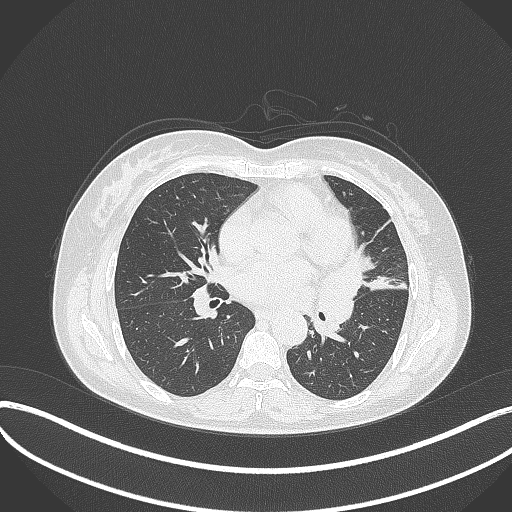
Chest CT, one axial slice; slice 173 of 373 in the series (ordered by position); reconstruction kernel B70f; 120 kVp; lung window (W 1500 / L -600 HU); 1 mm slice thickness; 512 × 512 image matrix. Patient: female, 54 years. From the clinical record (not read from this slice): clinical TNM (as recorded): T2a N1 M0; histopathological grade: G3.
Annotated regions visible in this slice (bounding box drawn by a radiologist):
- lung tumour (recorded histology: small cell carcinoma): bounding box (x1, y1, x2, y2) in pixels: (315, 260, 367, 328)